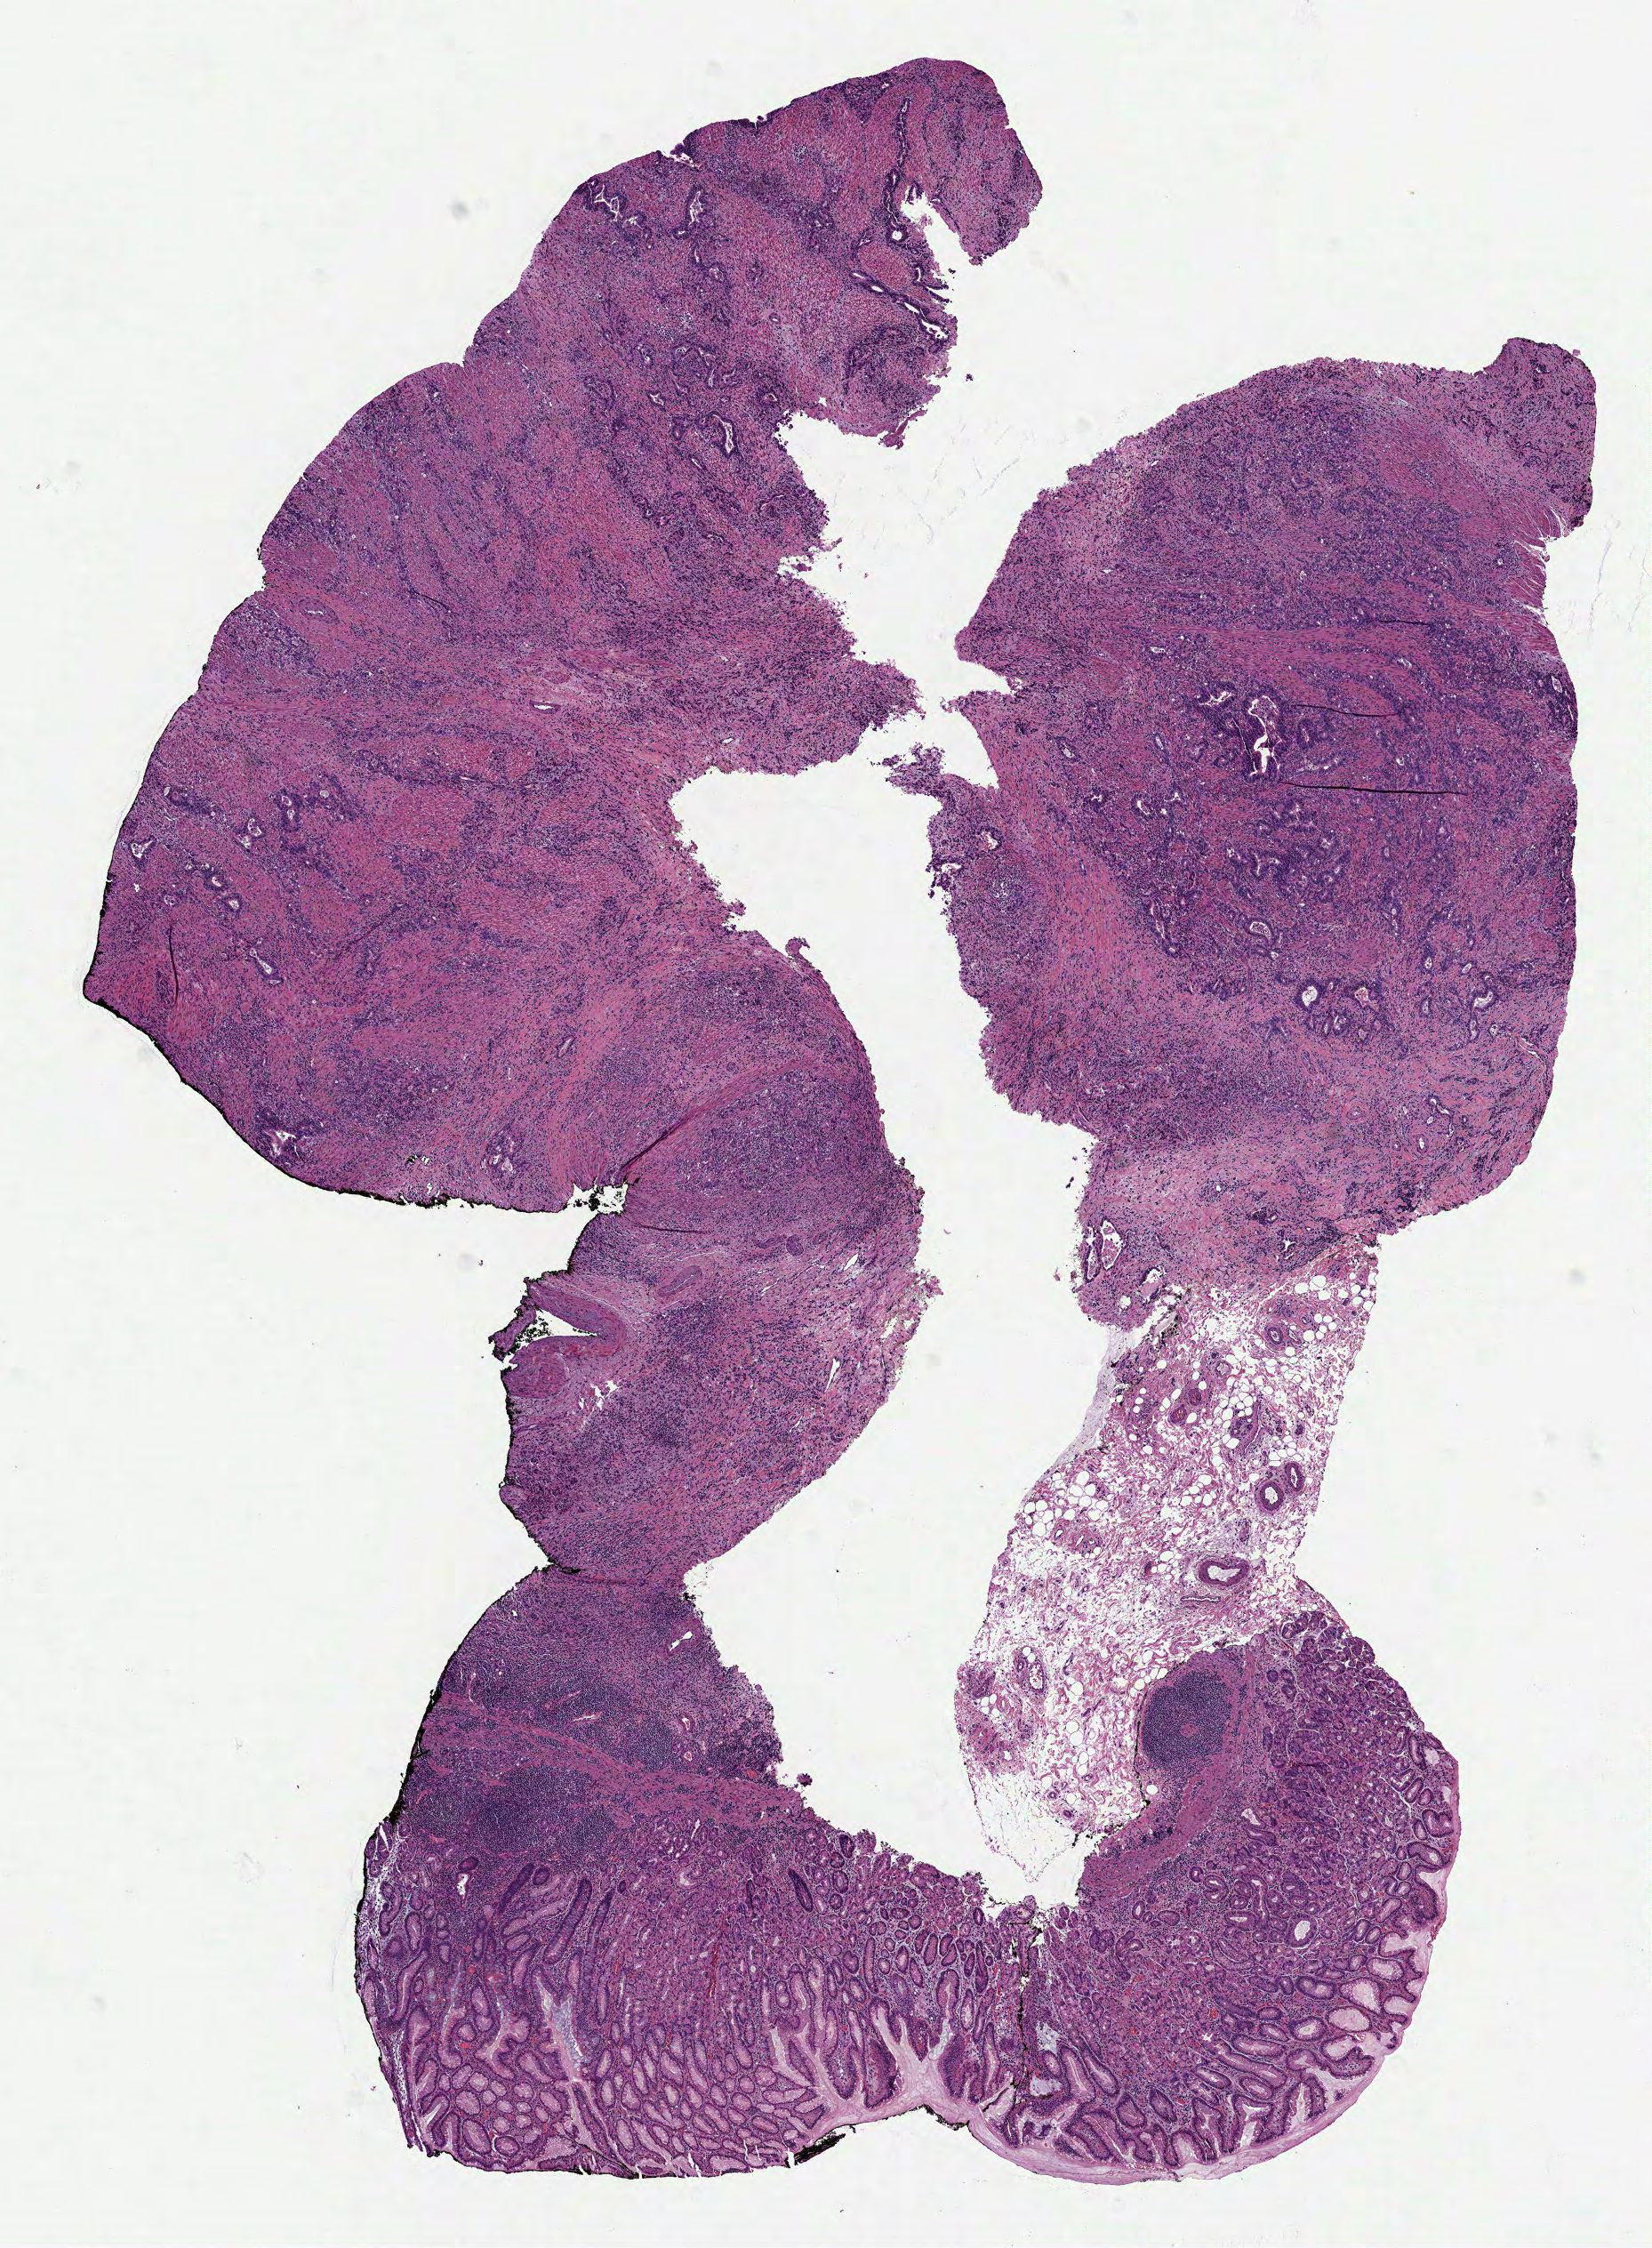
Digitized Hematoxylin and eosin (H&E) stained tissue section (whole slide), low-resolution overview of the scanned area, about 7.5 x 10.2 mm (acquisition: 40x scan); FFPE section; primary tumour sample from the stomach. Patient: male, age at initial diagnosis 77 years. Histologic grade: G3 (poorly differentiated).
- diagnosis: Carcinoma, diffuse type
- lymph nodes positive (case pathology): 10 of 20 examined
- AJCC pathologic stage: IIIC (7th edition)